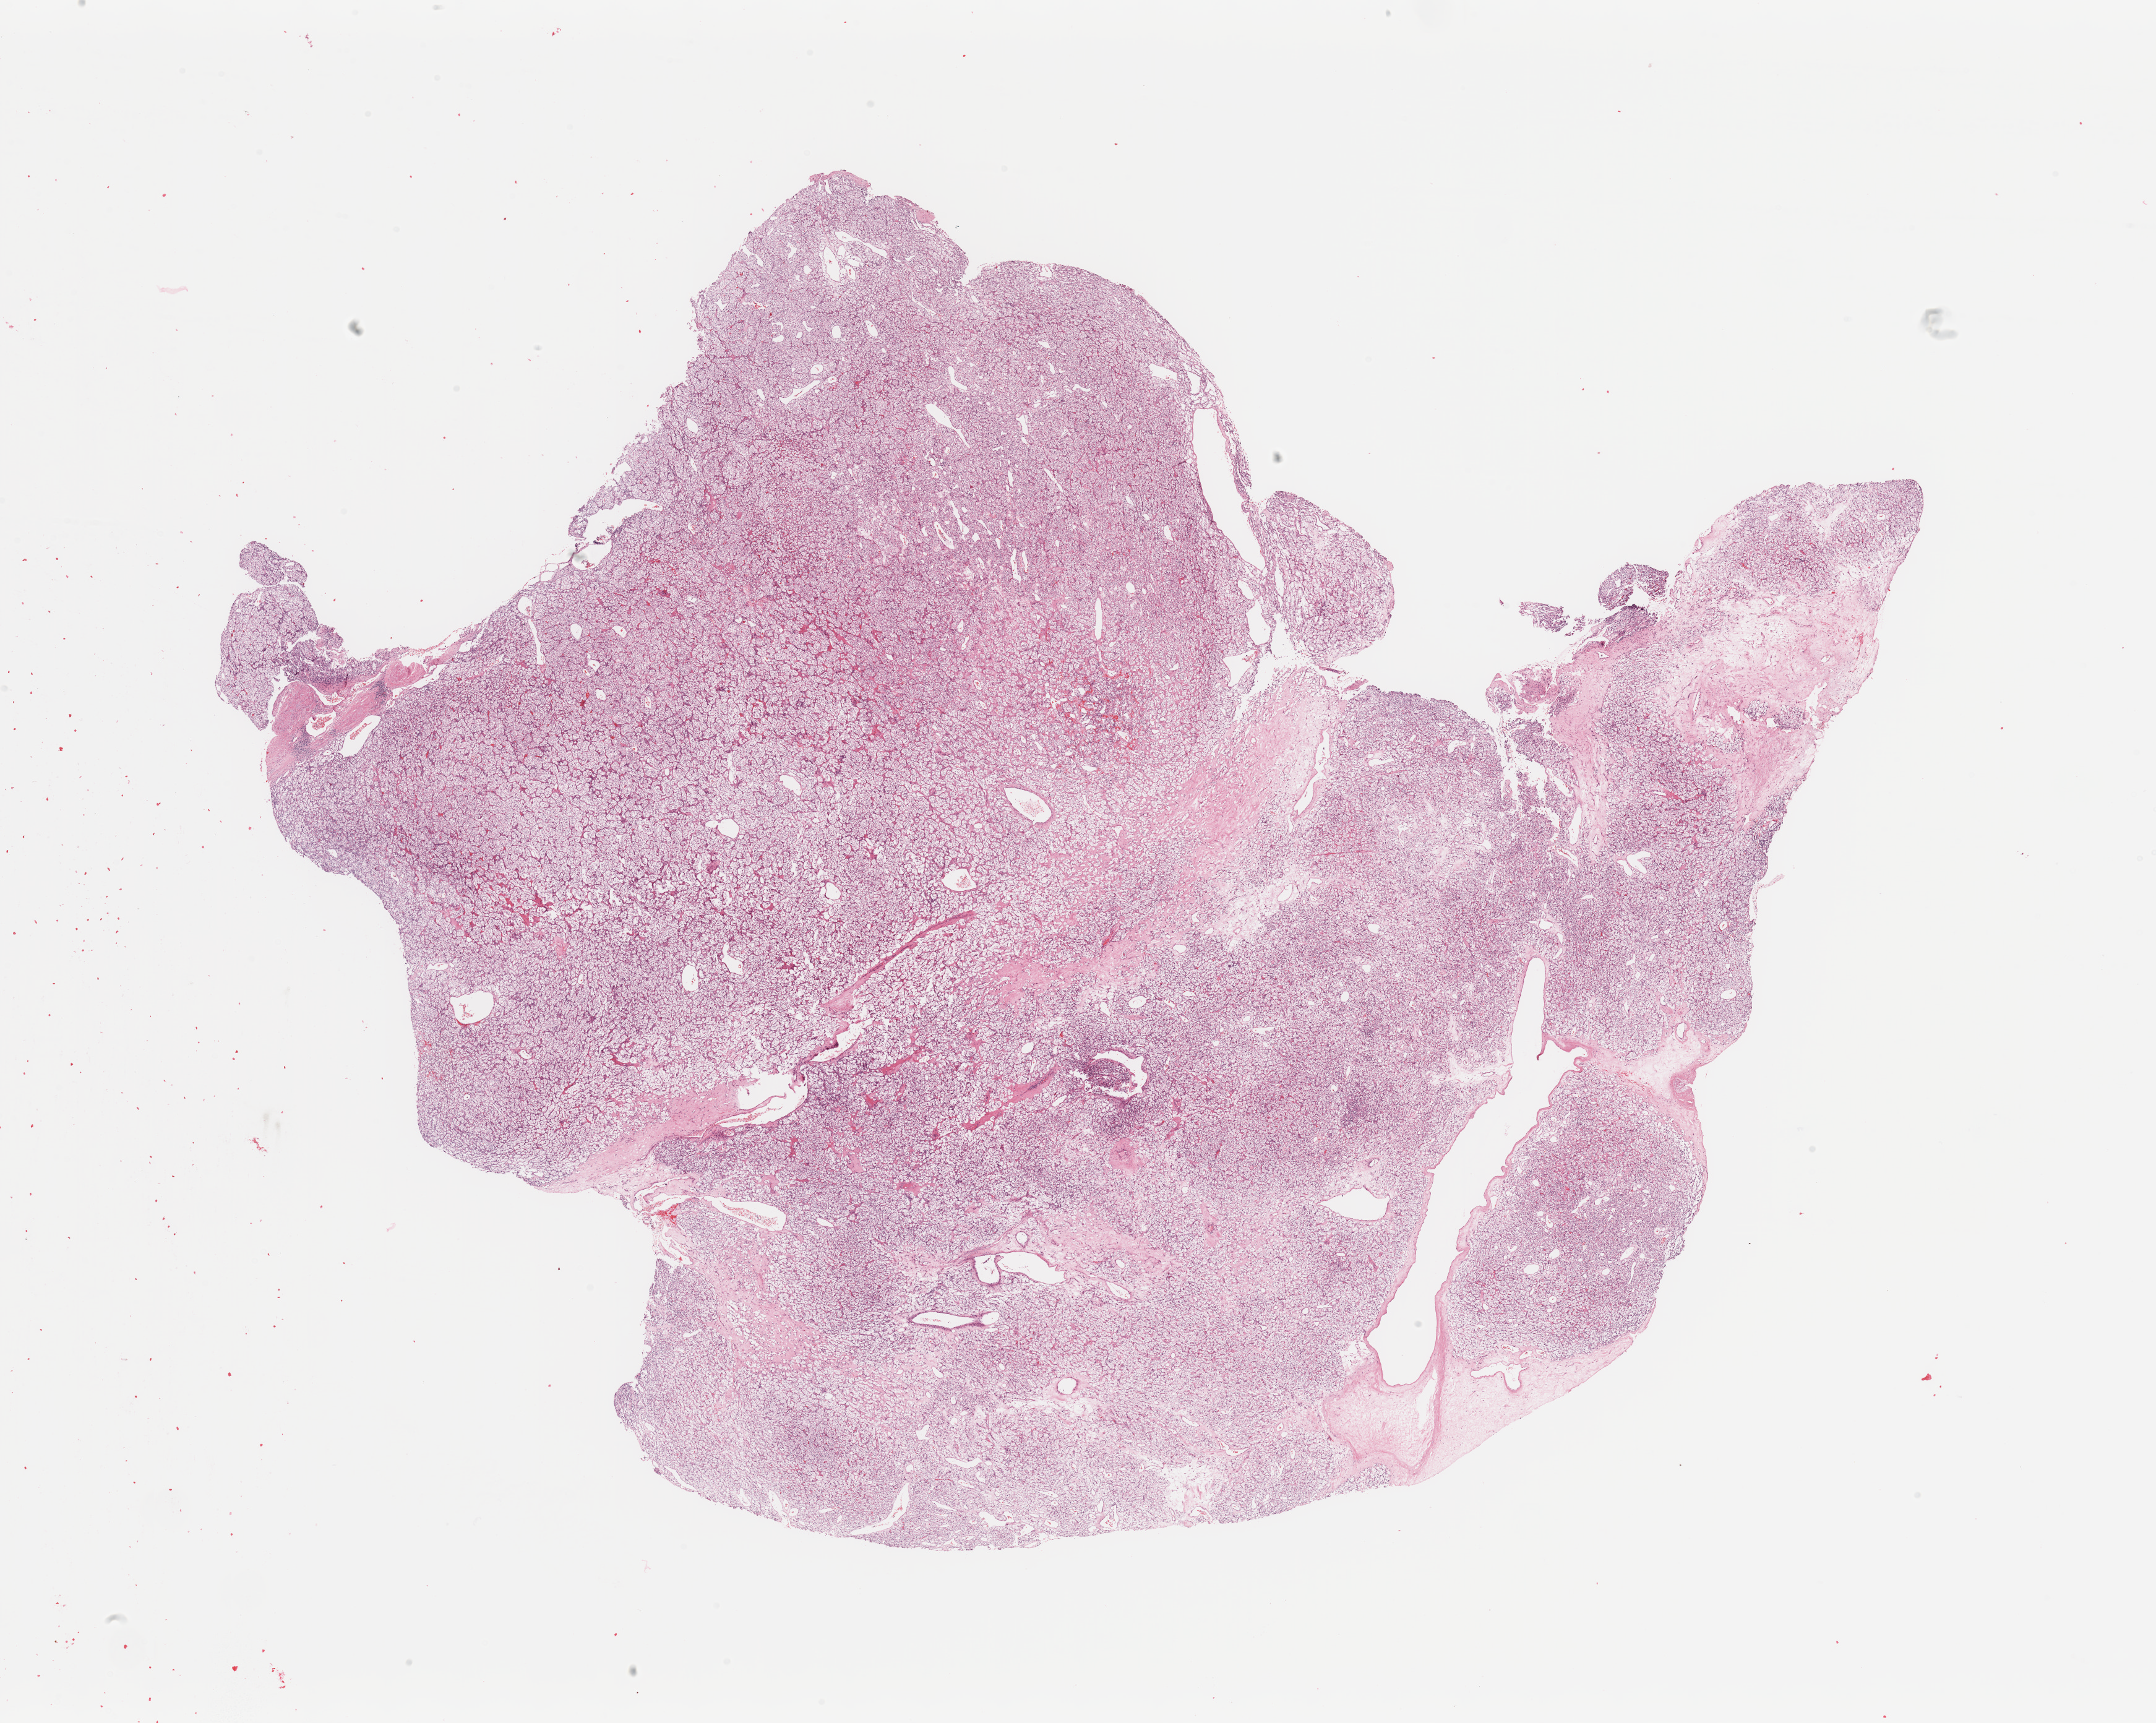
Hematoxylin and eosin (H&E) stained whole-slide image, shown as a low-resolution overview of the whole scanned area (about 27.6 x 22.0 mm); tumour tissue sample, sampled site: kidney. 69-year-old female patient. Histologic grade: G2 (moderately differentiated). Slide review estimates, as recorded: tumour nuclei 85%, necrosis 3%.
Histologic diagnosis: Renal cell carcinoma, NOS.